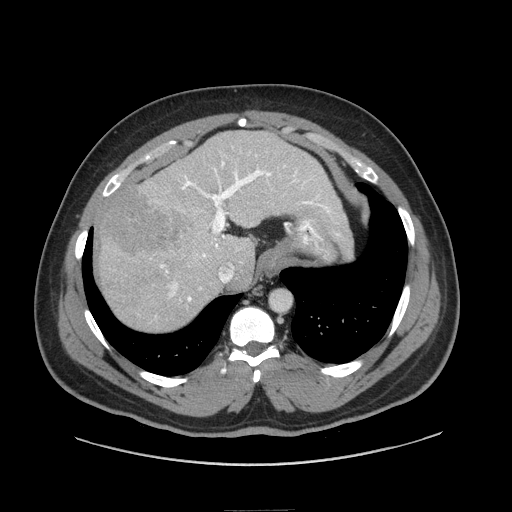
Contrast-enhanced abdominal CT (liver protocol), one axial slice. Slice 60 of 87 in the series (ordered by position). Reconstruction kernel STANDARD. Soft-tissue window (W 400 / L 40 HU). 512 × 512 image matrix. Case-level facts recorded for this patient, not image findings: diagnosis: hepatocellular carcinoma (patient treated with transarterial chemoembolisation; whether this scan precedes or follows treatment is not stated here); TNM stage (as recorded): Stage-II; Child-Pugh class: A; tumour differentiation: moderately differentiated.
Structures marked on this image (semi-automatically segmented with operator editing):
- liver parenchyma outside the tumour (the mass and vessels are separate outlines, so this box may not span the whole liver): bounding box (x1, y1, x2, y2) in pixels: (98, 132, 346, 330)
- mass: (98, 189, 183, 257)
- liver vessels: (160, 161, 331, 302)